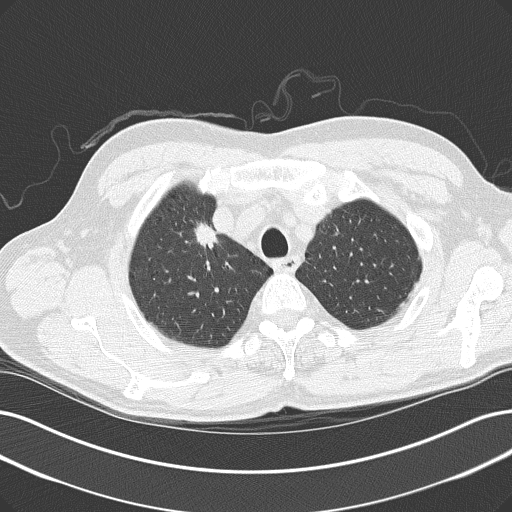
Axial slice from a low-dose chest CT screening exam. Baseline annual screen. Lung window (W 1500 / L -600 HU). 2 mm slice thickness. Lung (sharp) reconstruction kernel (B50f). Slice 29 of 152 in the series. Male, age 61 years at enrolment.
Expert reader's lesion annotation, bounding box [x1, y1, x2, y2] px = [190, 222, 246, 268]. The screening reader recorded 2 non-calcified nodules or masses ≥4 mm on this exam (right upper lobe, right upper lobe); which of them this box marks is not recorded. Participant outcome: lung cancer diagnosed 54 days after this screen — adenocarcinoma, NOS, right upper lobe, poorly differentiated (G3), stage IIIB (AJCC 6th edition).